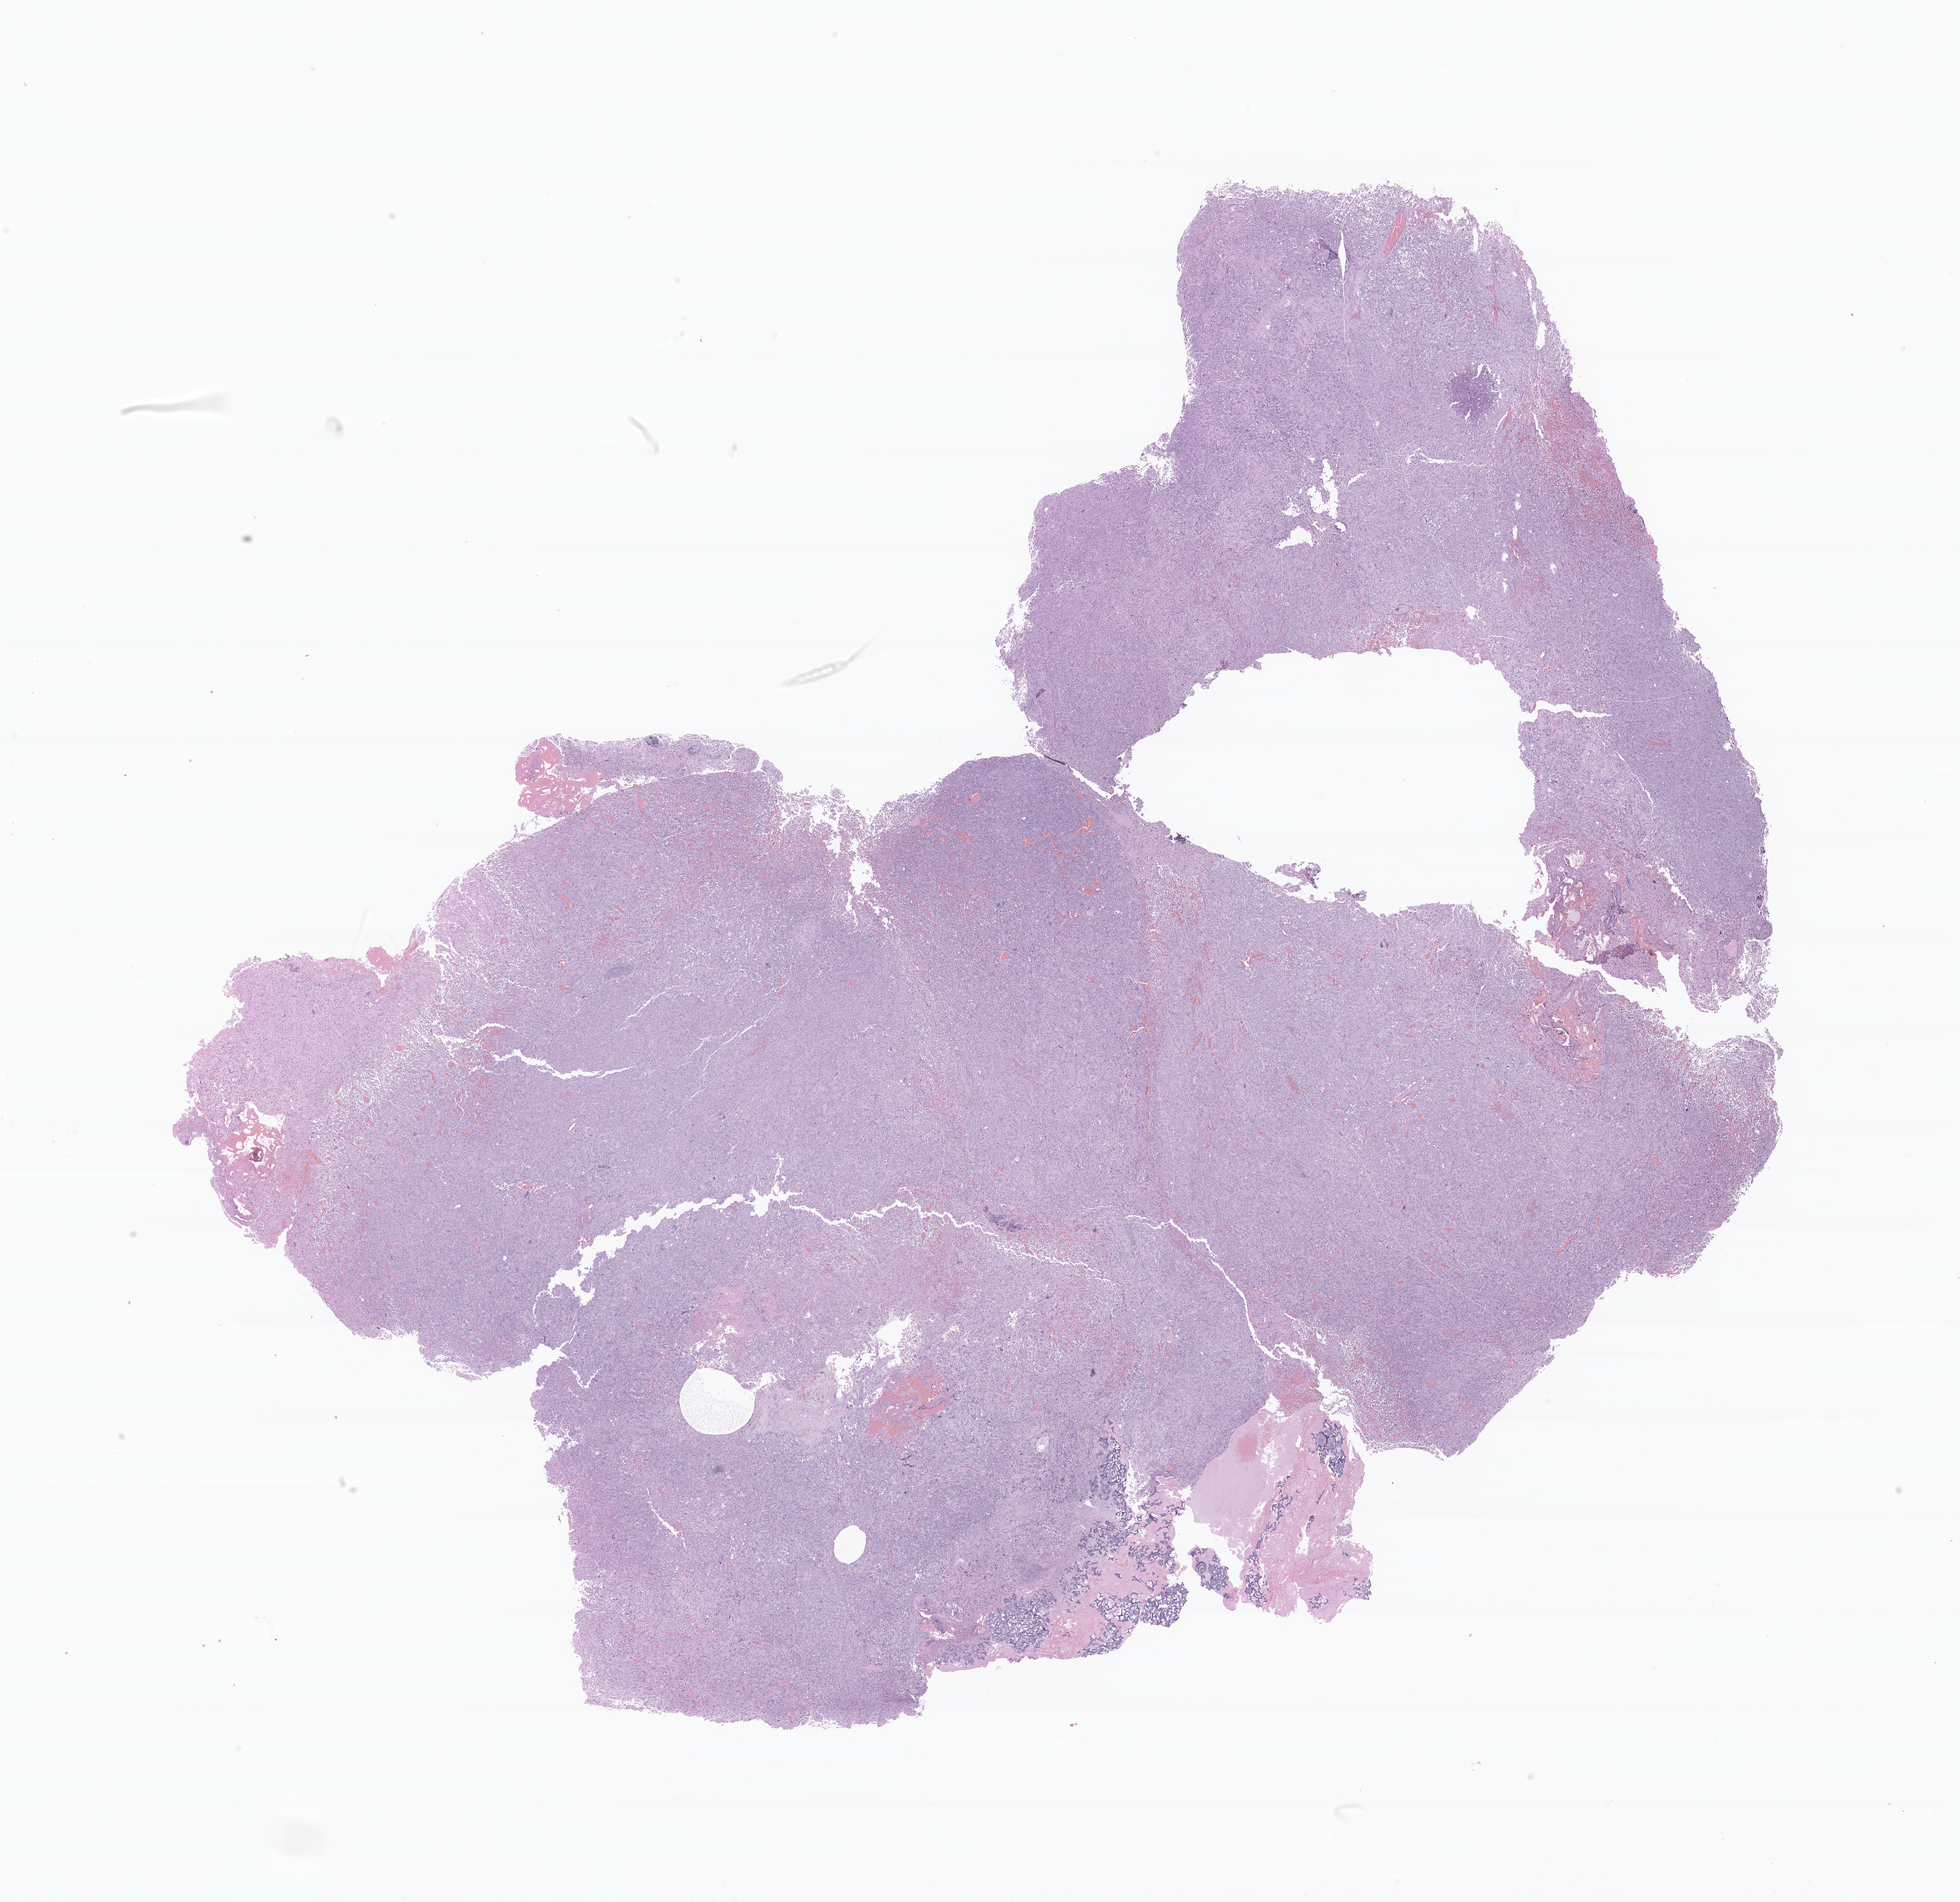
Digitized H&E-stained section of tumor tissue from the temporal lobe — a low-resolution overview of the entire scanned area, about 21.7 x 21.0 mm; formalin-fixed paraffin-embedded section. Male patient, age 147 months (12 years 3 months).
Diagnosis (ICD-O-3 morphology term): Glioma, malignant.